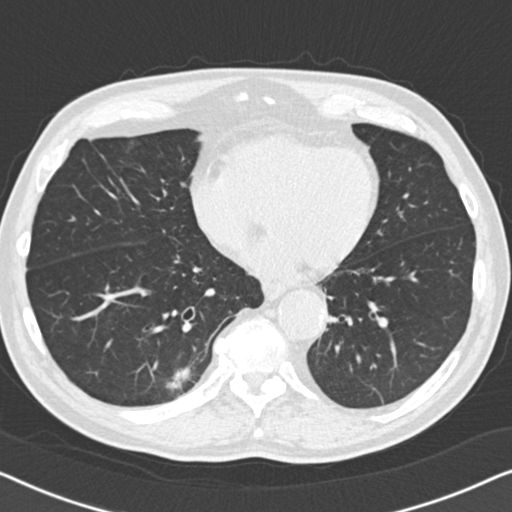
Low-dose screening chest CT, one axial slice; position 51 of 164 along the scan axis; reconstruction kernel B30f; lung window (W 1500 / L -600 HU); 512 × 512 image matrix, field of view 330 × 330 mm.
Annotated regions visible in this slice (outlined manually by an expert reader):
- lesion 1 (tumor, lower lobe of right lung): bounding box [x1, y1, x2, y2] px = [166, 366, 191, 391]